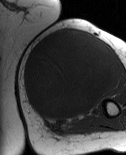
MRI of an extremity soft-tissue mass, one axial slice; MR volume resampled by the dataset authors to the PET/CT grid (not the native acquisition matrix); 3.27 mm slice thickness; 126 × 155 image matrix, field of view 123 × 151 mm. Female patient. From the clinical record (not read from this slice): histological type: pleiomorphic leiomyosarcoma; grade: high; site of the primary tumour: left biceps.
Outlined on this slice (expert contour drawn on MRI and transferred to this co-registered scan by the dataset authors):
- gross tumour volume including surrounding oedema: bounding box (x1, y1, x2, y2) in pixels: (22, 28, 114, 121)
- gross tumour volume (mass): (22, 31, 114, 119)